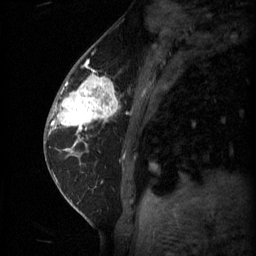
Breast MRI (dynamic contrast-enhanced), one sagittal slice. Slice 20 of 60 in the series (ordered by position). 3 images stored at this slice position (order not interpretable as contrast timing). 1.5 T. TE 4.2 ms, TR 11 ms. 2 mm slice thickness. 256 × 256 image matrix, field of view 180 × 180 mm. Female patient, age 62 years.
Annotated regions visible in this slice (semi-automatic segmentation, software-assisted and operator-edited):
- analysis volume of interest (the breast-tissue region the enhancement analysis was run in; not a lesion): bounding box <55,72,120,135> (left, top, right, bottom; pixels)
- tumour enhancement mask (voxels above the 70 % enhancement threshold inside the analysis volume of interest): <55,74,119,131>